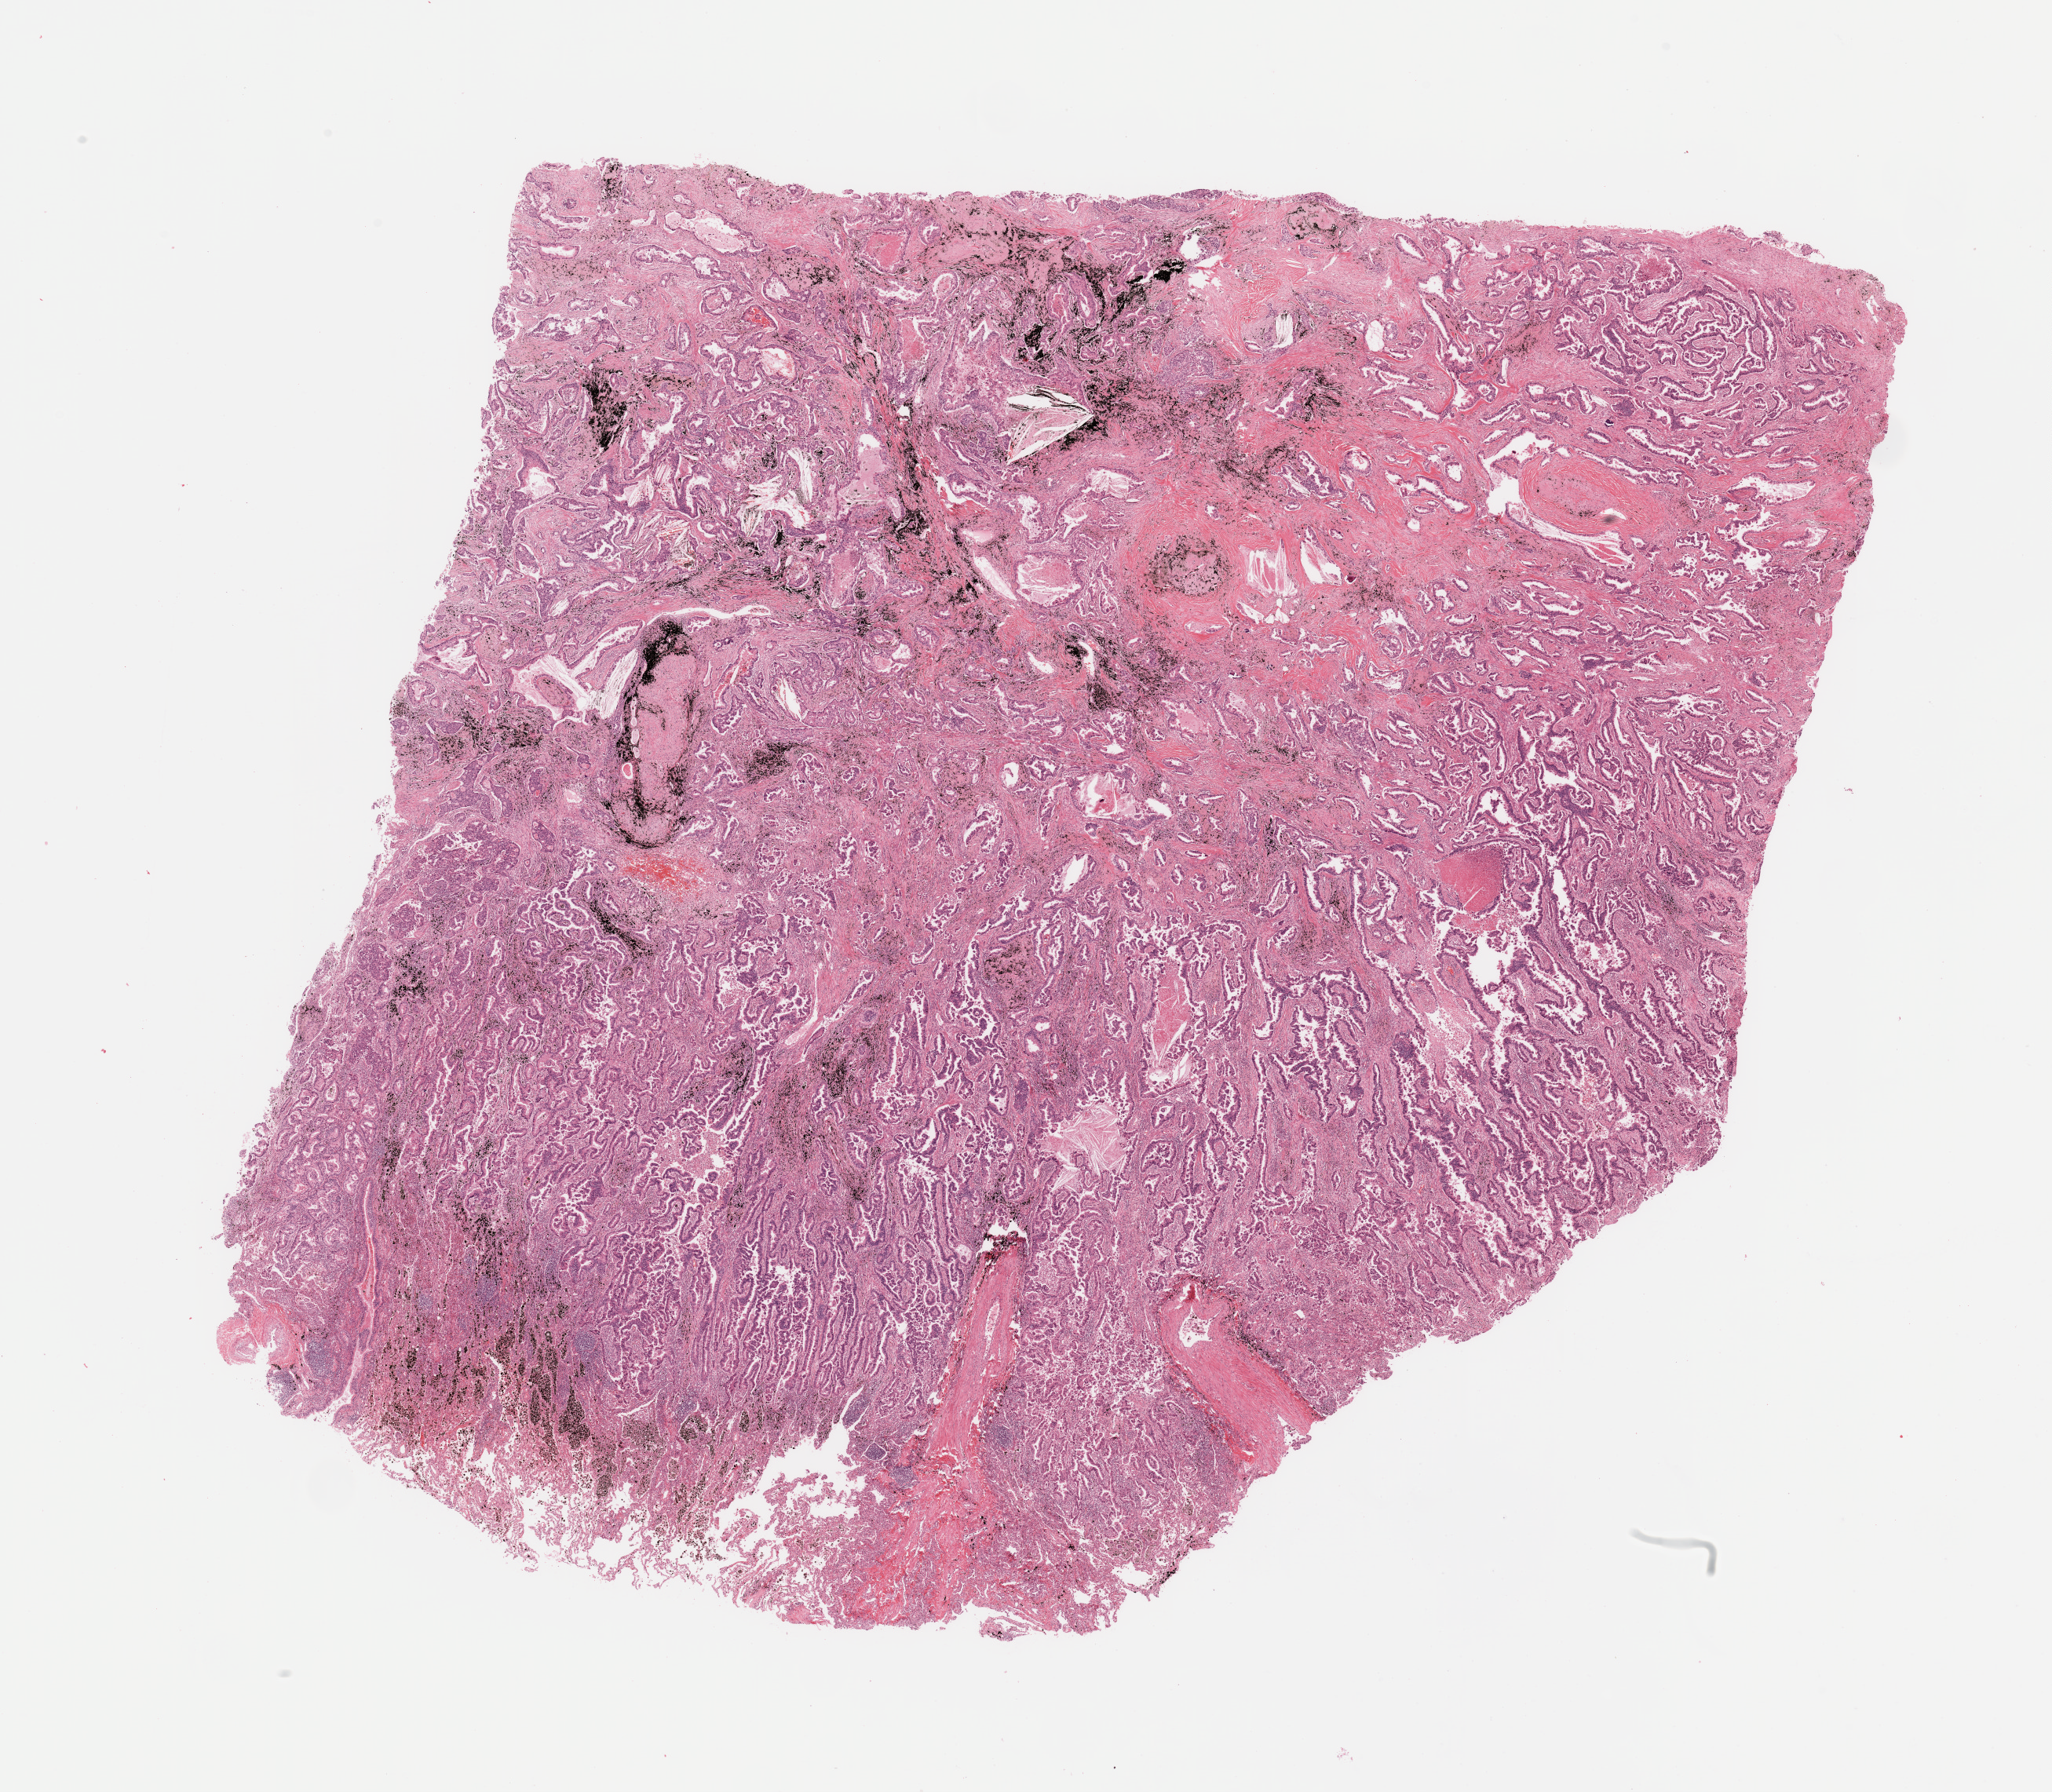
Whole-slide histology image, H&E-stained — shown as a low-resolution overview of the whole scanned area (about 20.7 x 18.1 mm), lung, tumour tissue. Patient: male, age 60 years. Histologic grade: G2 (moderately differentiated).
* histologic diagnosis: Adenocarcinoma, NOS
* AJCC pathologic stage: IIA